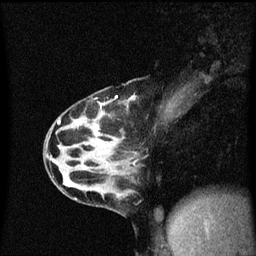
Breast MRI (dynamic contrast-enhanced), one sagittal slice. Slice 24 of 60 in the series (ordered by position). Dynamic contrast-enhanced series, image 2 of 3 at this slice position (ordered by acquisition). 1.5 T. TE 4.2 ms, TR 8.4 ms. 2 mm slice thickness. 256 × 256 image matrix, field of view 200 × 200 mm. Patient: female, 32 years.
Outlined on this slice (semi-automatic segmentation, software-assisted and operator-edited):
- analysis volume of interest (the breast-tissue region the enhancement analysis was run in; not a lesion): bounding box <55,80,173,167> (left, top, right, bottom; pixels)
- tumour enhancement mask (voxels above the 70 % enhancement threshold inside the analysis volume of interest): <60,96,136,121>